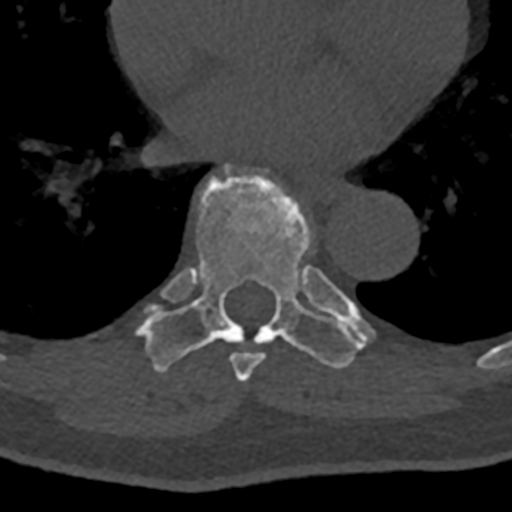
CT including the spine, one axial slice. Reconstruction kernel Br40s/3. 120 kVp. Bone window (W 1800 / L 400 HU). 0.5 mm slice thickness. 512 × 512 image matrix, field of view 160 × 160 mm. Male patient, age 74 years. From the clinical record (not read from this slice): primary cancer: renal; vertebrae with lytic lesions (as recorded): T10, L1, L2, L3, L4, L5.
Structures marked on this image (semi-automatic segmentation, software-assisted and operator-edited):
- T7 vertebra: bounding box [x1, y1, x2, y2] px = [221, 170, 349, 382]
- T8 vertebra: [136, 162, 374, 372]